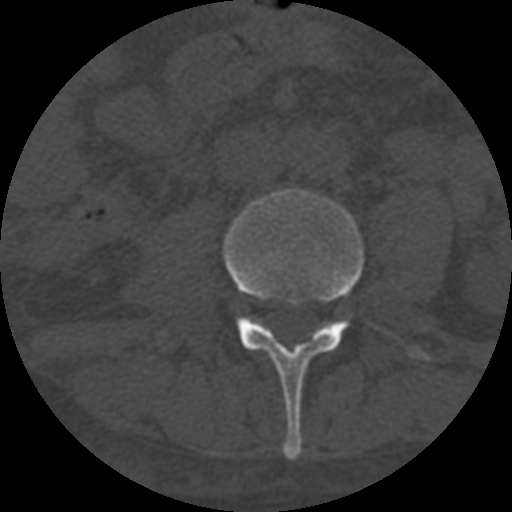
CT including the spine, one axial slice. One of 3 acquisitions stored at this slice position. Bone window (W 1800 / L 400 HU). 1.25 mm slice thickness. 512 × 512 image matrix, field of view 160 × 160 mm. Patient age 55 years. From the clinical record (not read from this slice): primary cancer: colon; vertebrae with lytic lesions (as recorded): T12, L1, L5.
Annotated regions visible in this slice (semi-automatic segmentation, software-assisted and operator-edited):
- L3 vertebra: box from (x=223, y=189) to (x=429, y=460) px